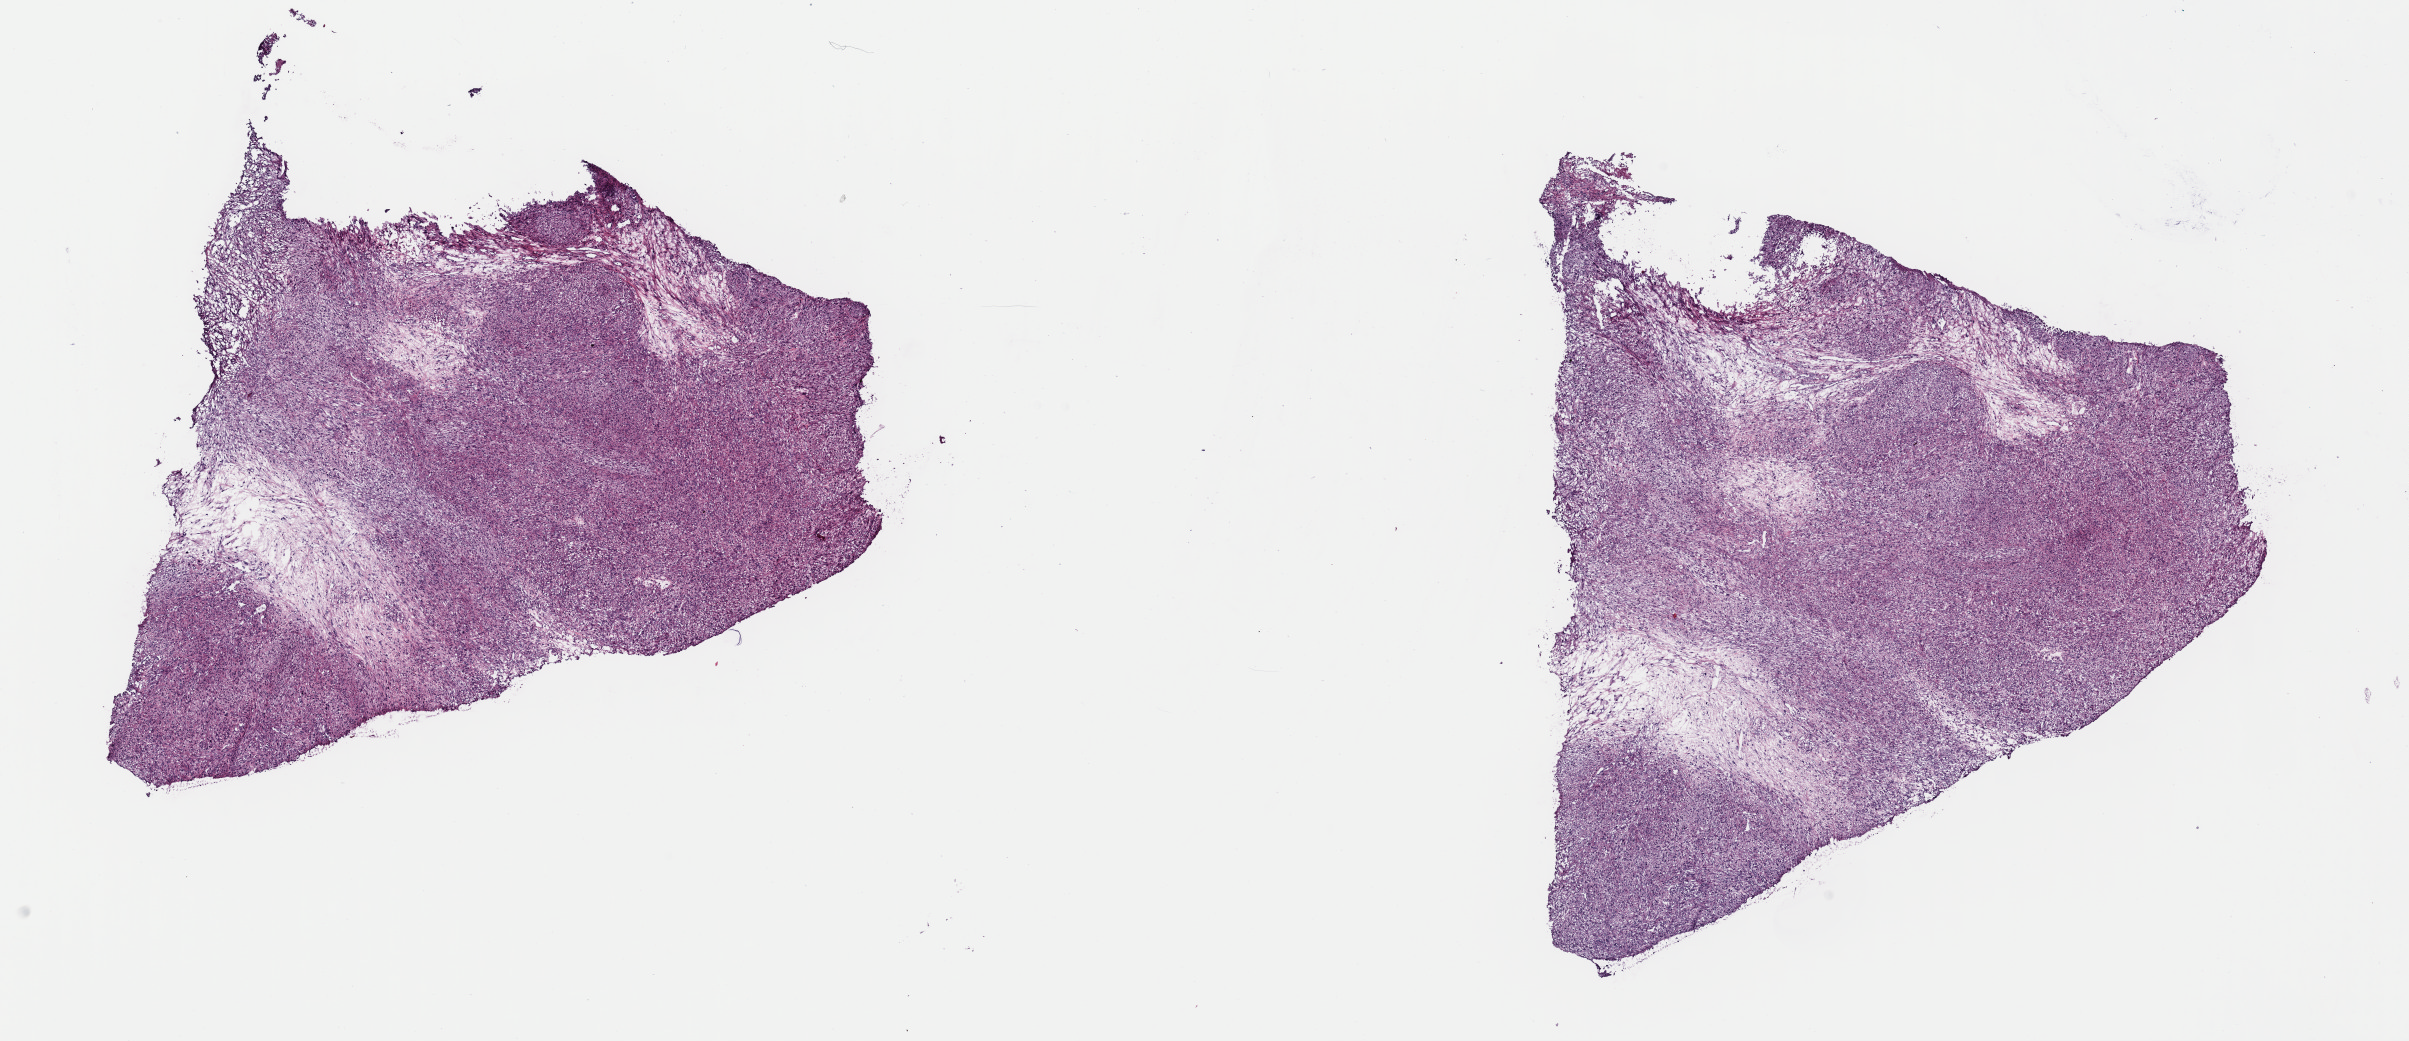
Digitized Hematoxylin and eosin (H&E) stained tissue section (whole slide), whole scanned area (about 19.0 x 8.2 mm) shown as a low-resolution overview, frozen section, bones, joints and articular cartilage of limbs, primary tumour sample. Male, age 80 years at initial diagnosis. Pathologist review of this section (percent, as recorded): tumour cells 85%, tumour nuclei 100%, normal cells 0%, stromal cells 15%, necrosis 0%. Infiltration values recorded for this section: lymphocyte infiltration 0%, monocyte infiltration 0%, neutrophil infiltration 0%.
Pathologic diagnosis: Leiomyosarcoma, NOS (long bones of lower limb and associated joints).